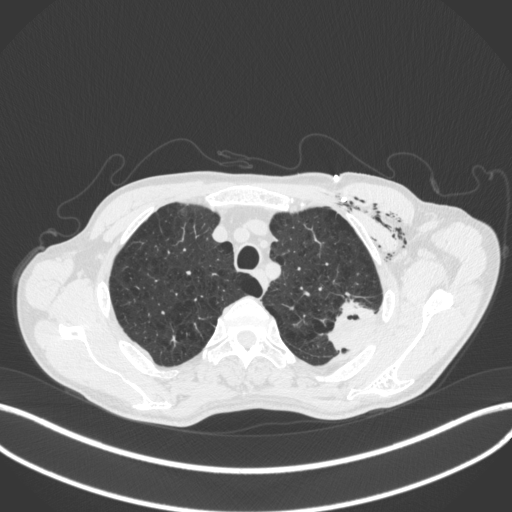
Chest CT, one axial slice; position 339 of 416 along the scan axis; reconstruction kernel B31f; lung window (W 1500 / L -600 HU); 1 mm slice thickness; 512 × 512 image matrix, field of view 400 × 400 mm. Patient: male, 58 years. From the clinical record (not read from this slice): clinical TNM (as recorded): T3 N0 M0.
Annotated regions visible in this slice (rectangle marked by the reading radiologist):
- lung tumour (recorded histology: adenocarcinoma): bounding box [x1, y1, x2, y2] px = [323, 295, 380, 356]